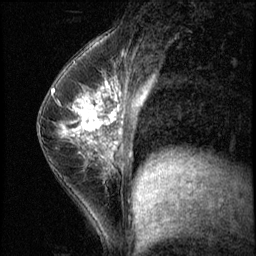
Breast MRI (dynamic contrast-enhanced), one sagittal slice. Slice 32 of 56 in the series (ordered by position). 3 images stored at this slice position (order not interpretable as contrast timing). 1.5 T. TE 4.2 ms, TR 8.7 ms. 256 × 256 image matrix. Female patient, age 35 years. From the clinical record (not read from this slice): setting: breast cancer imaged before/during neoadjuvant chemotherapy; receptor status: HER2-positive.
Outlined on this slice (semi-automatic segmentation, software-assisted and operator-edited):
- analysis volume of interest (the breast-tissue region the enhancement analysis was run in; not a lesion): box from (x=58, y=84) to (x=138, y=186) px
- tumour enhancement mask (voxels above the 140 % enhancement threshold inside the analysis volume of interest): (x=61, y=84)–(x=138, y=142)